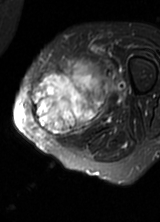
MRI of an extremity soft-tissue mass, one axial slice. Slice 22 of 69 in the series (ordered by position). T2-weighted fat-saturated. MR volume resampled by the dataset authors to the PET/CT grid (not the native acquisition matrix). 3.27 mm slice thickness. 160 × 222 image matrix, field of view 156 × 217 mm. Female patient. Case-level facts recorded for this patient, not image findings: histological type: pleomorphic leiomyosarcoma; grade: high; site of the primary tumour: left thigh.
Outlined on this slice (expert contour drawn on MRI and transferred to this co-registered scan by the dataset authors):
- gross tumour volume including surrounding oedema: bounding box <32,59,115,137> (left, top, right, bottom; pixels)
- gross tumour volume (mass): <32,73,105,137>